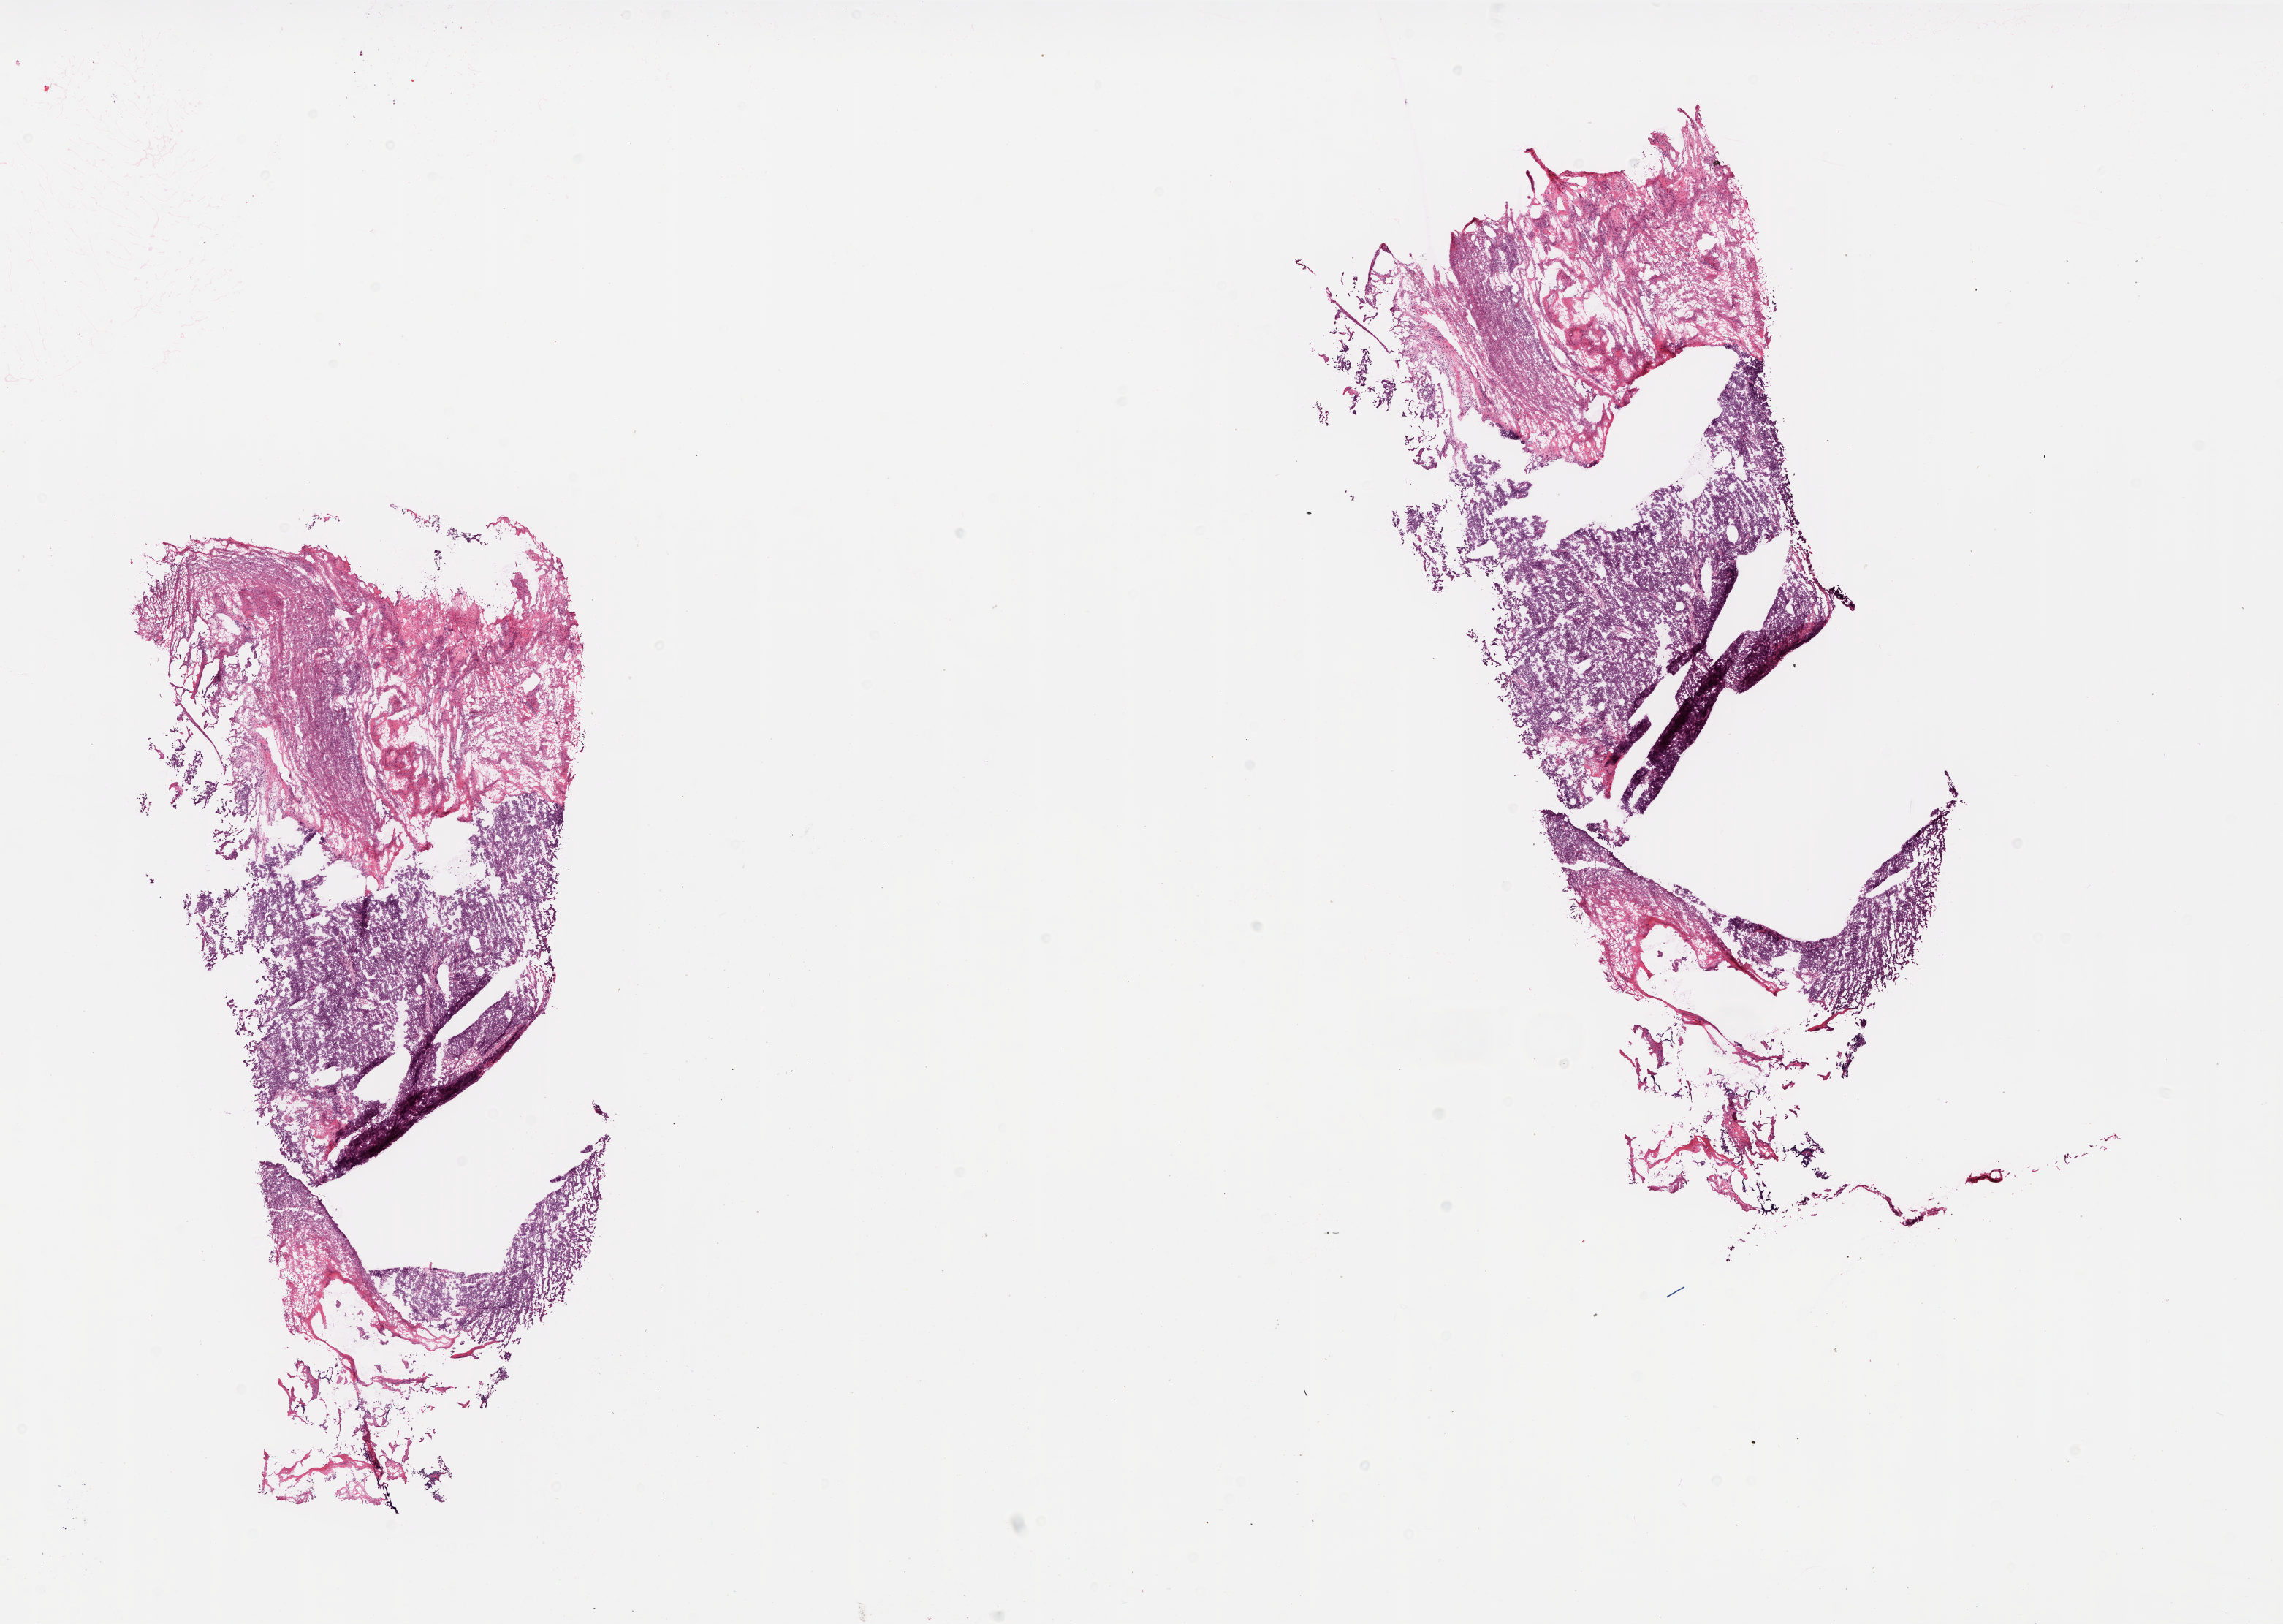
Hematoxylin and eosin (H&E) stained whole-slide image — shown as a low-resolution overview of the whole scanned area (about 25.0 x 17.7 mm), frozen section from the top of the tissue portion, sample: primary tumour, ovary. Female, age 69 years at initial diagnosis. Histologic grade: G3 (poorly differentiated). Composition of this section per pathologist review: tumour cells 90%, tumour nuclei 95%, normal cells 0%, stromal cells 10%, necrosis 0%.
Histologic diagnosis: Serous cystadenocarcinoma, NOS. FIGO stage: IV.